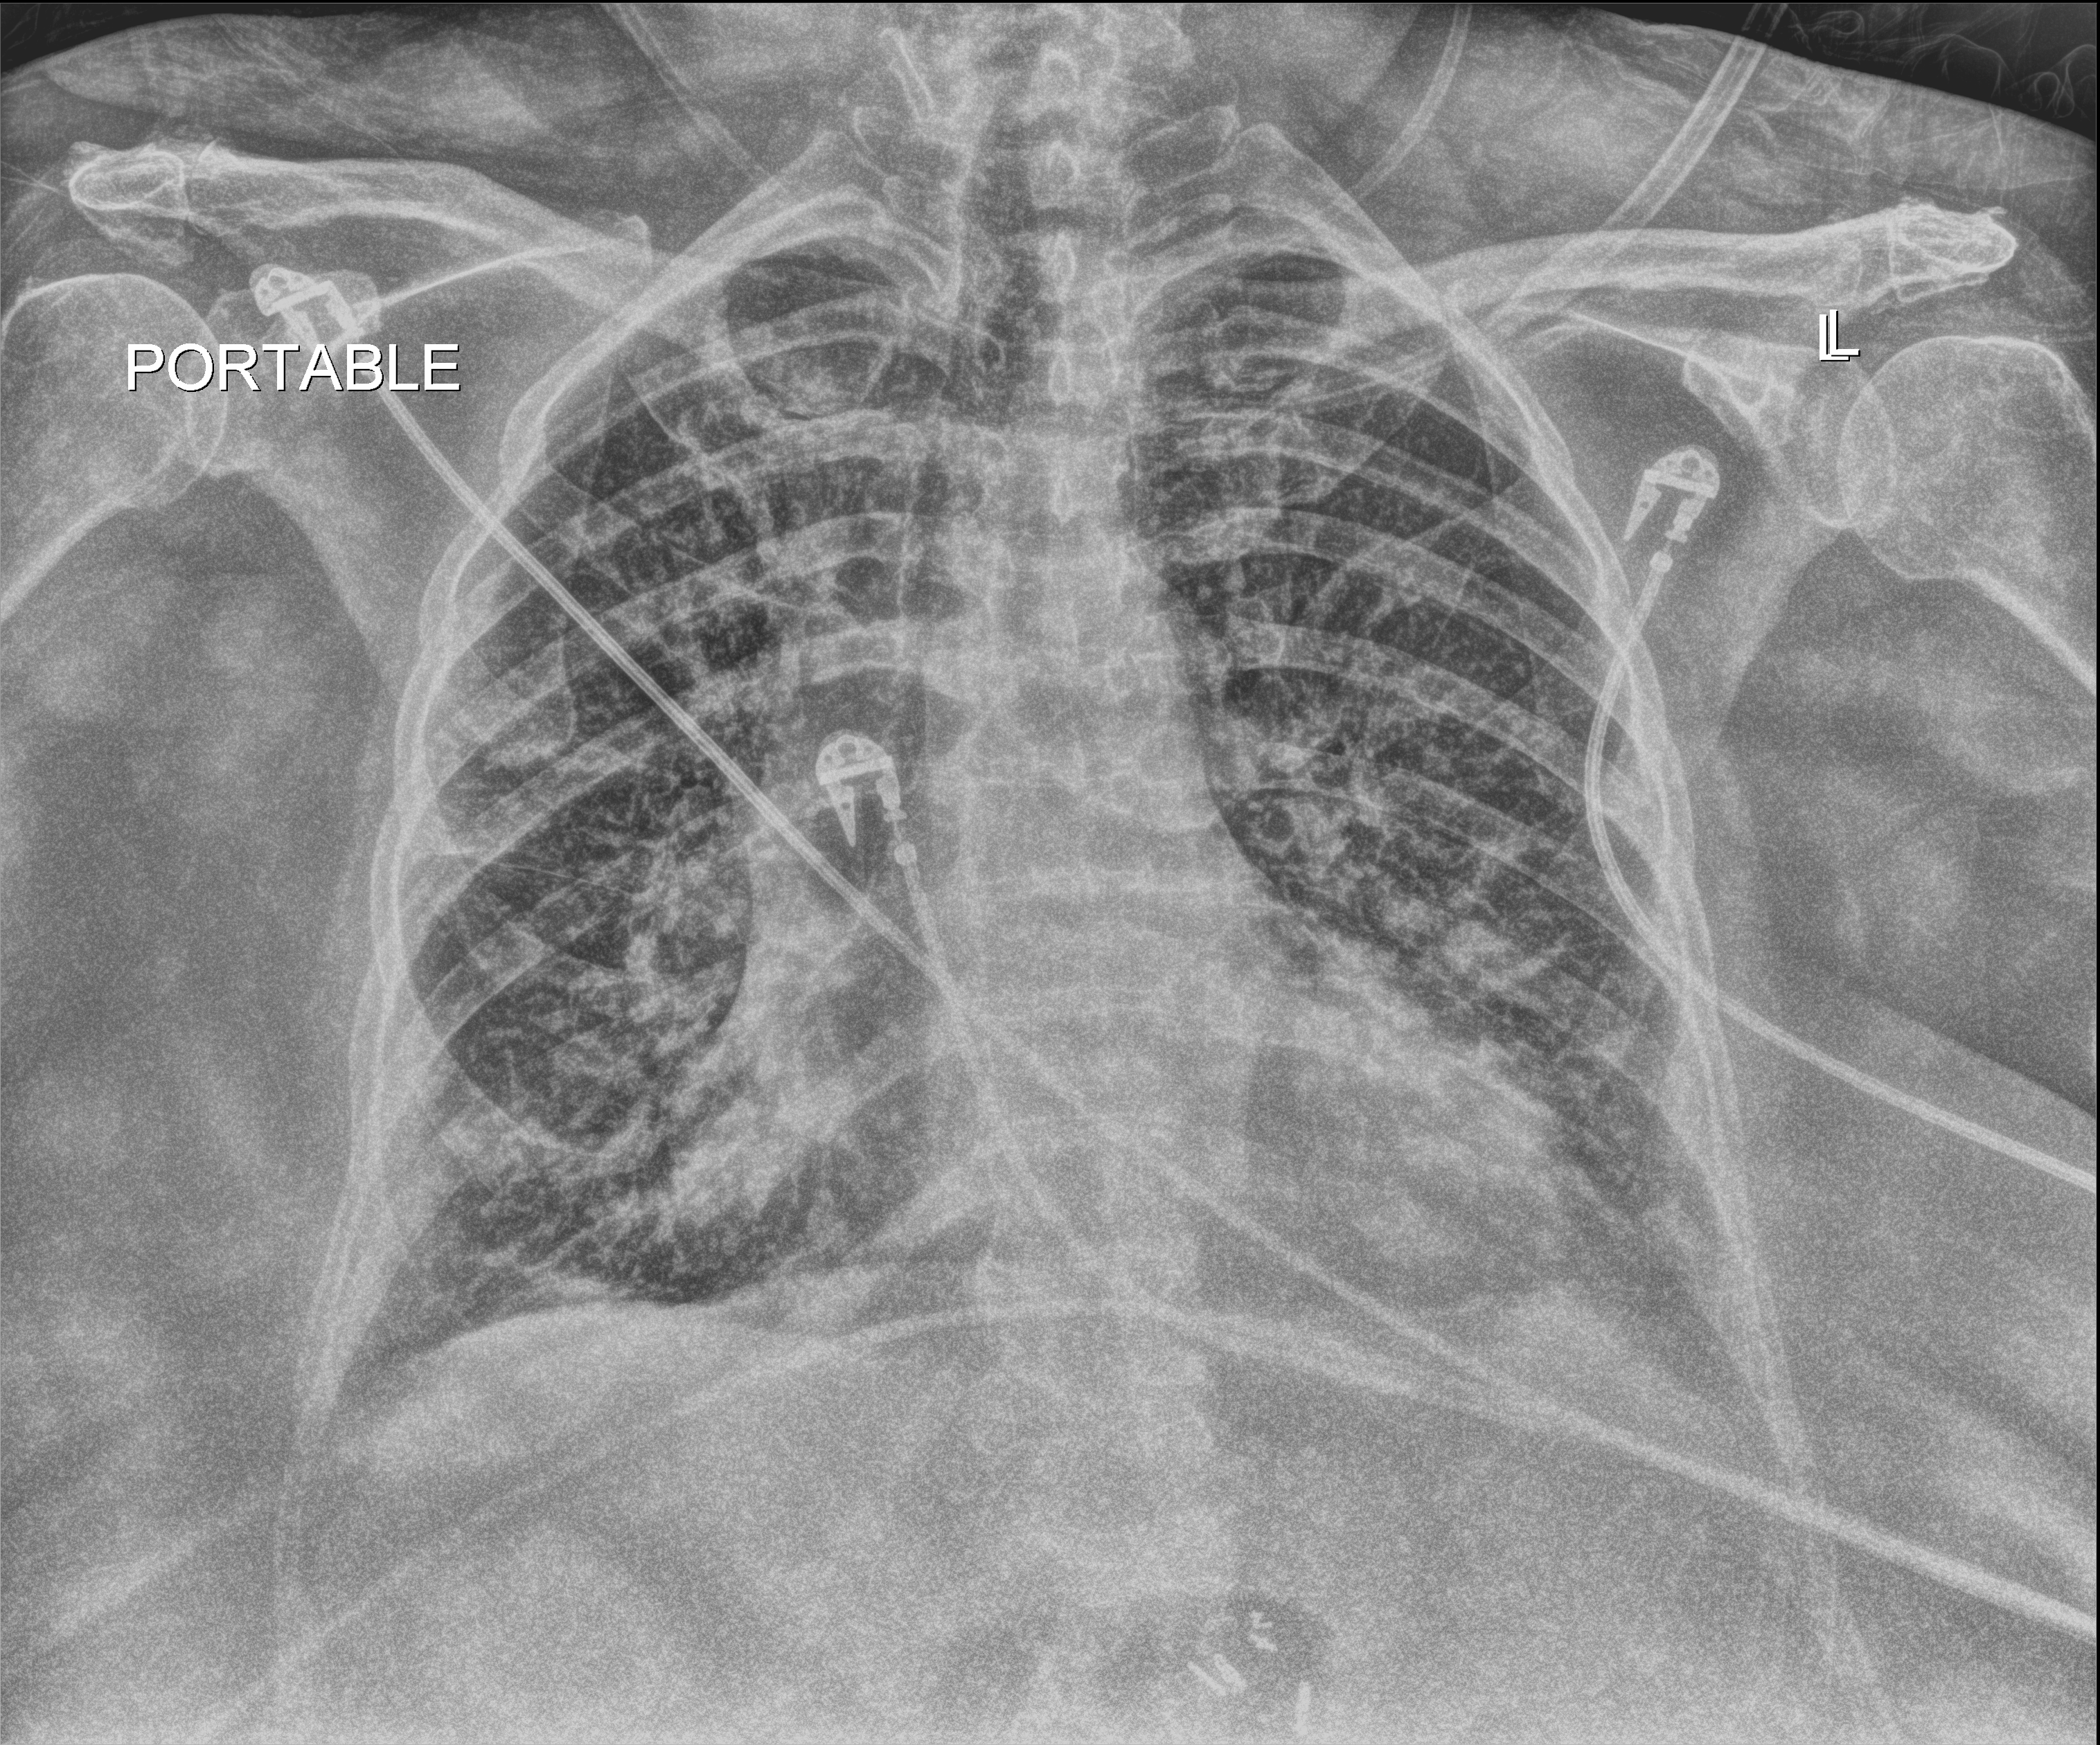
Portable chest radiograph. Female patient hospitalised with COVID-19, age 75–90 years.
Hospital-stay facts (about this admission, not read from this image; timing relative to this image not recorded):
- admitted to intensive care during this hospital stay: no
- mechanically ventilated during this hospital stay: no